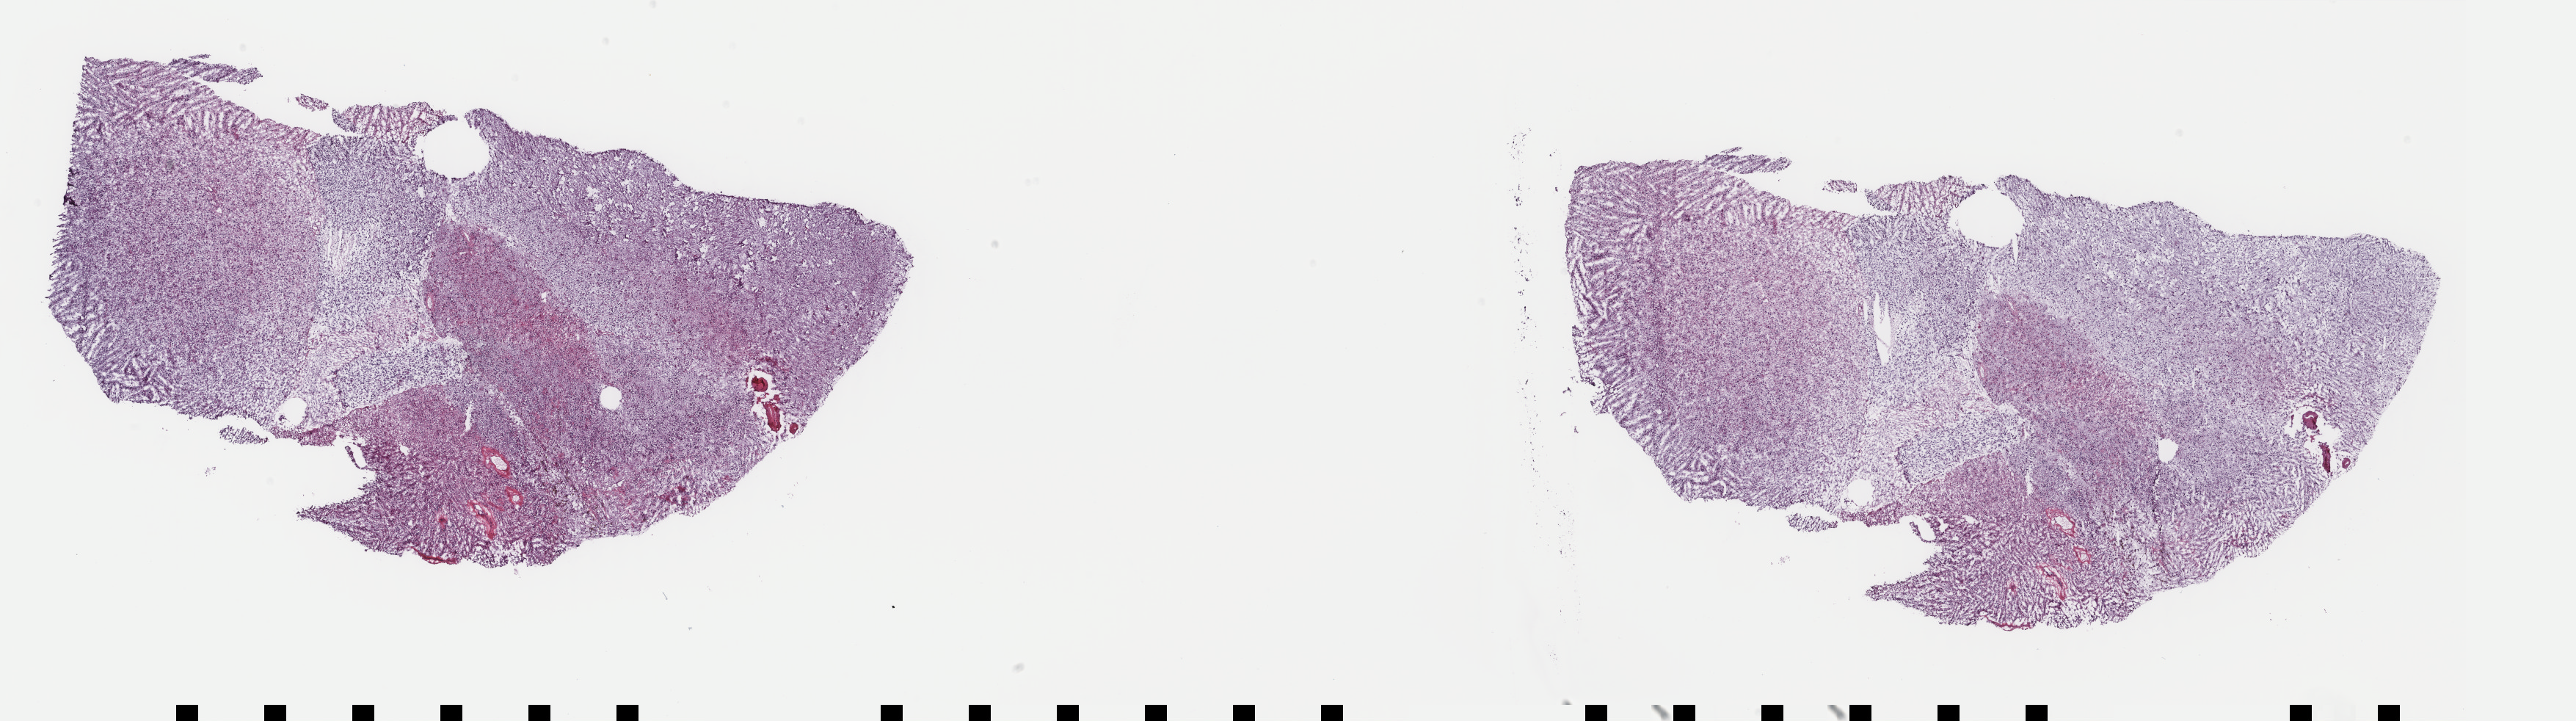
Whole-slide histology image, H&E — whole scanned area (about 27.9 x 7.8 mm) shown as a low-resolution overview; frozen section from the top of the tissue portion; primary tumour sample from the brain. Female patient; age at initial diagnosis 62 years. Histologic grade: G2 (moderately differentiated). Composition of this section per pathologist review: tumour cells 75%, tumour nuclei 70%, normal cells 10%, stromal cells 15%, necrosis 0%. Inflammatory infiltration, as recorded: lymphocyte infiltration 0%, monocyte infiltration 0%, neutrophil infiltration 0%.
* pathologic diagnosis: Astrocytoma, NOS (cerebrum)